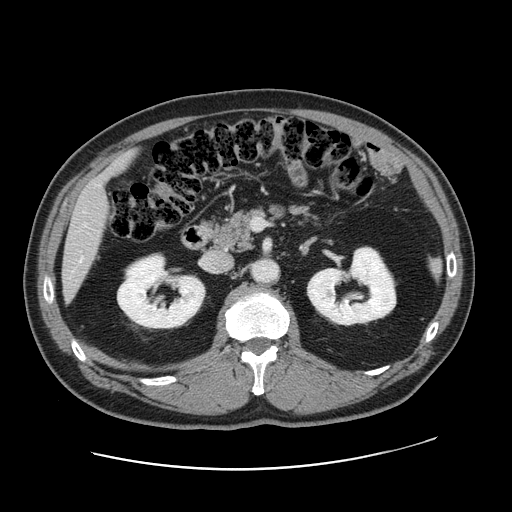
Contrast-enhanced abdominal CT, one axial slice. 120 kVp. Intravenous contrast given. Soft-tissue window (W 400 / L 40 HU). 2.5 mm slice thickness. 512 × 512 image matrix, field of view 403 × 403 mm. Male patient, age 63 years. Case-level facts recorded for this patient, not image findings: diagnosis: colorectal cancer liver metastases, imaged before liver resection.
Annotated regions visible in this slice (expert manual segmentation):
- hepatic veins: bounding box [x1, y1, x2, y2] px = [80, 258, 82, 260]
- liver: [63, 158, 128, 296]
- planned liver remnant (the part of the liver to remain after resection): [114, 157, 127, 167]